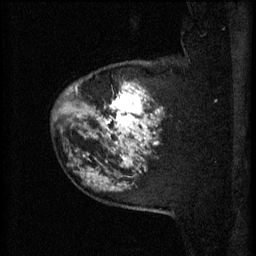
Breast MRI (dynamic contrast-enhanced), one sagittal slice. Slice 50 of 60 in the series (ordered by position). 3 images stored at this slice position (order not interpretable as contrast timing). 1.5 T. TE 4.2 ms, TR 11 ms. 2 mm slice thickness. 256 × 256 image matrix, field of view 180 × 180 mm. Female patient, age 52 years.
Annotated regions visible in this slice (semi-automatic segmentation, software-assisted and operator-edited):
- analysis volume of interest (the breast-tissue region the enhancement analysis was run in; not a lesion): bounding box <81,62,164,157> (left, top, right, bottom; pixels)
- tumour enhancement mask (voxels above the 70 % enhancement threshold inside the analysis volume of interest): <81,82,164,157>